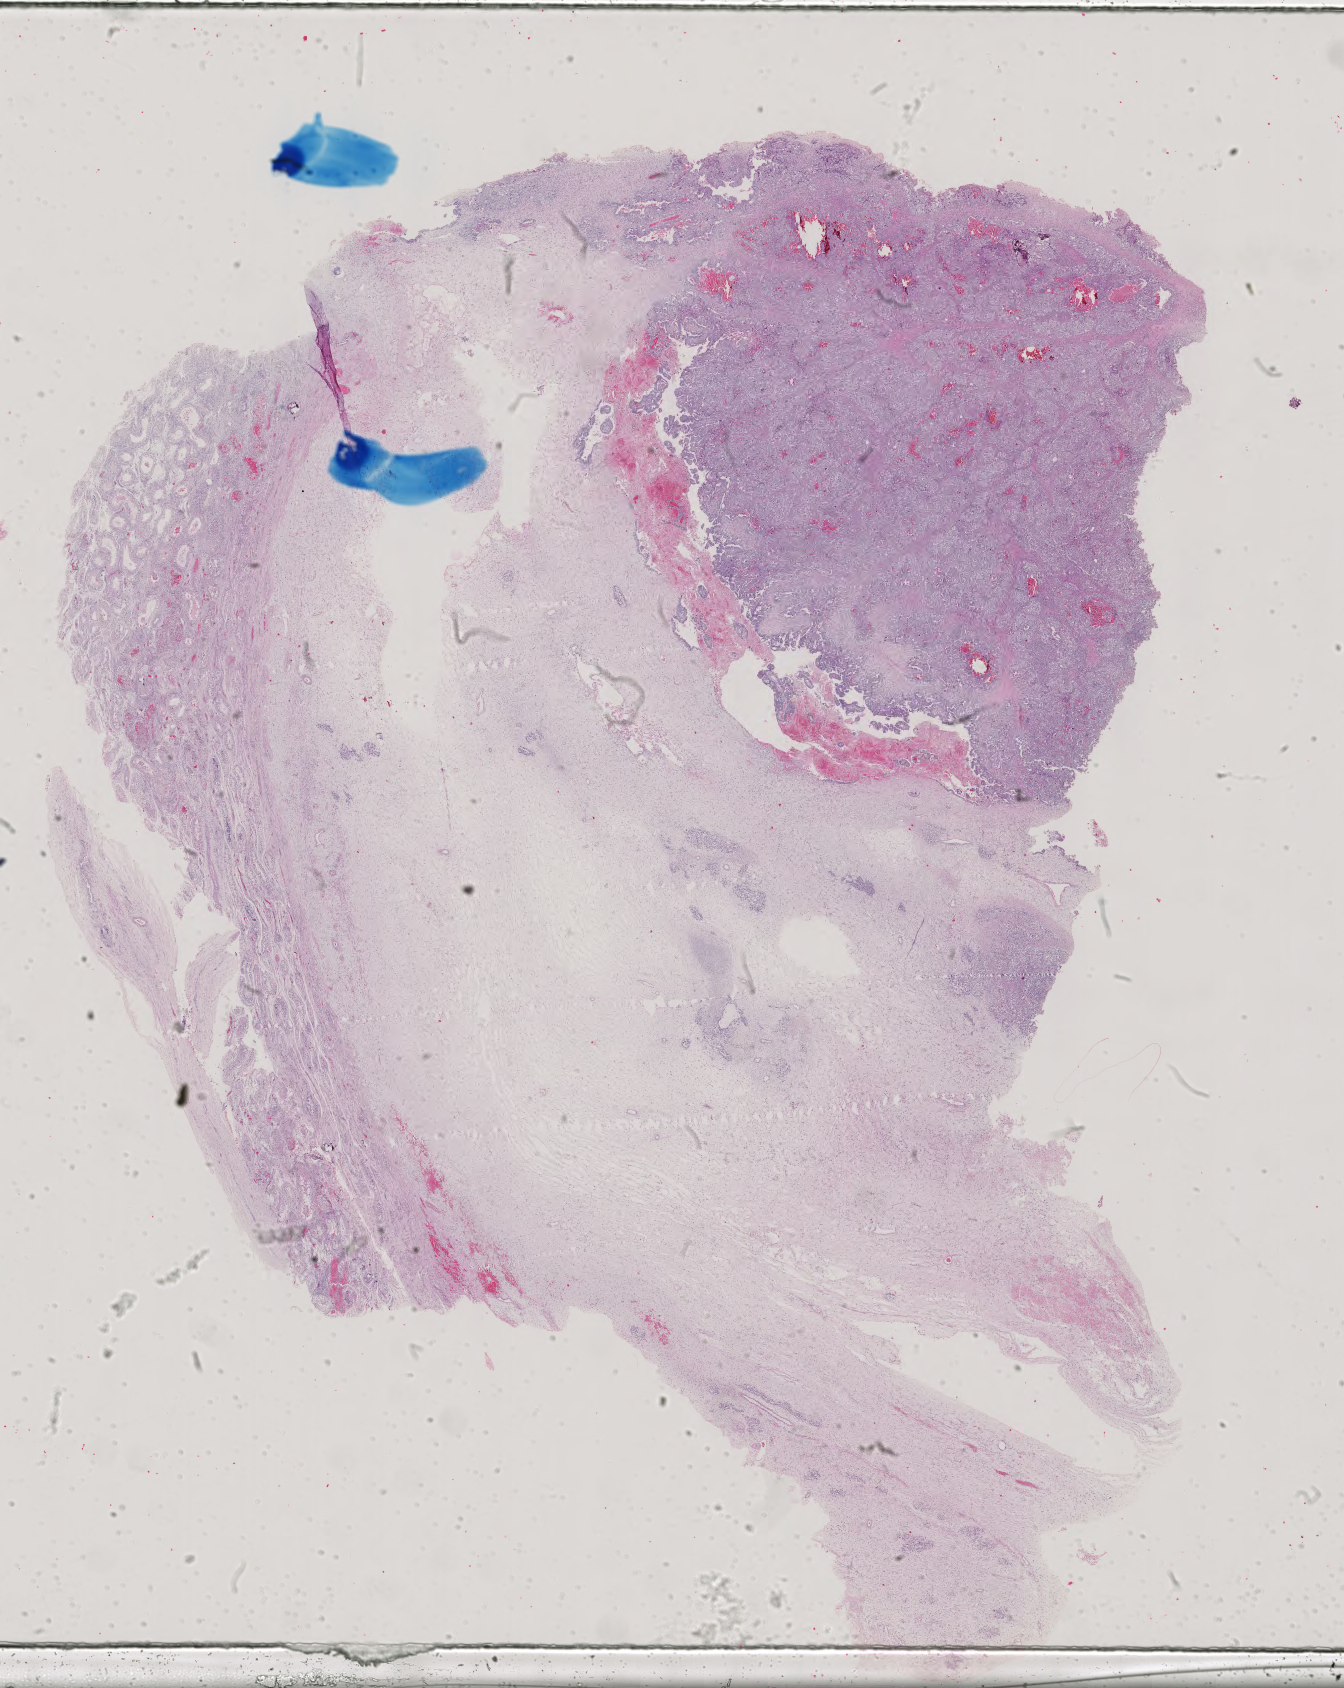
Hematoxylin and eosin (H&E) stained whole-slide image — whole scanned area (about 19.6 x 24.6 mm, acquisition: 40x scan) shown as a low-resolution overview, FFPE section, sample: primary tumour, testis. Male, age 21 years at initial diagnosis.
- pathologic diagnosis: Embryonal carcinoma, NOS
- AJCC pathologic stage: IS
- TNM: T1 N0 M0
- laterality: left